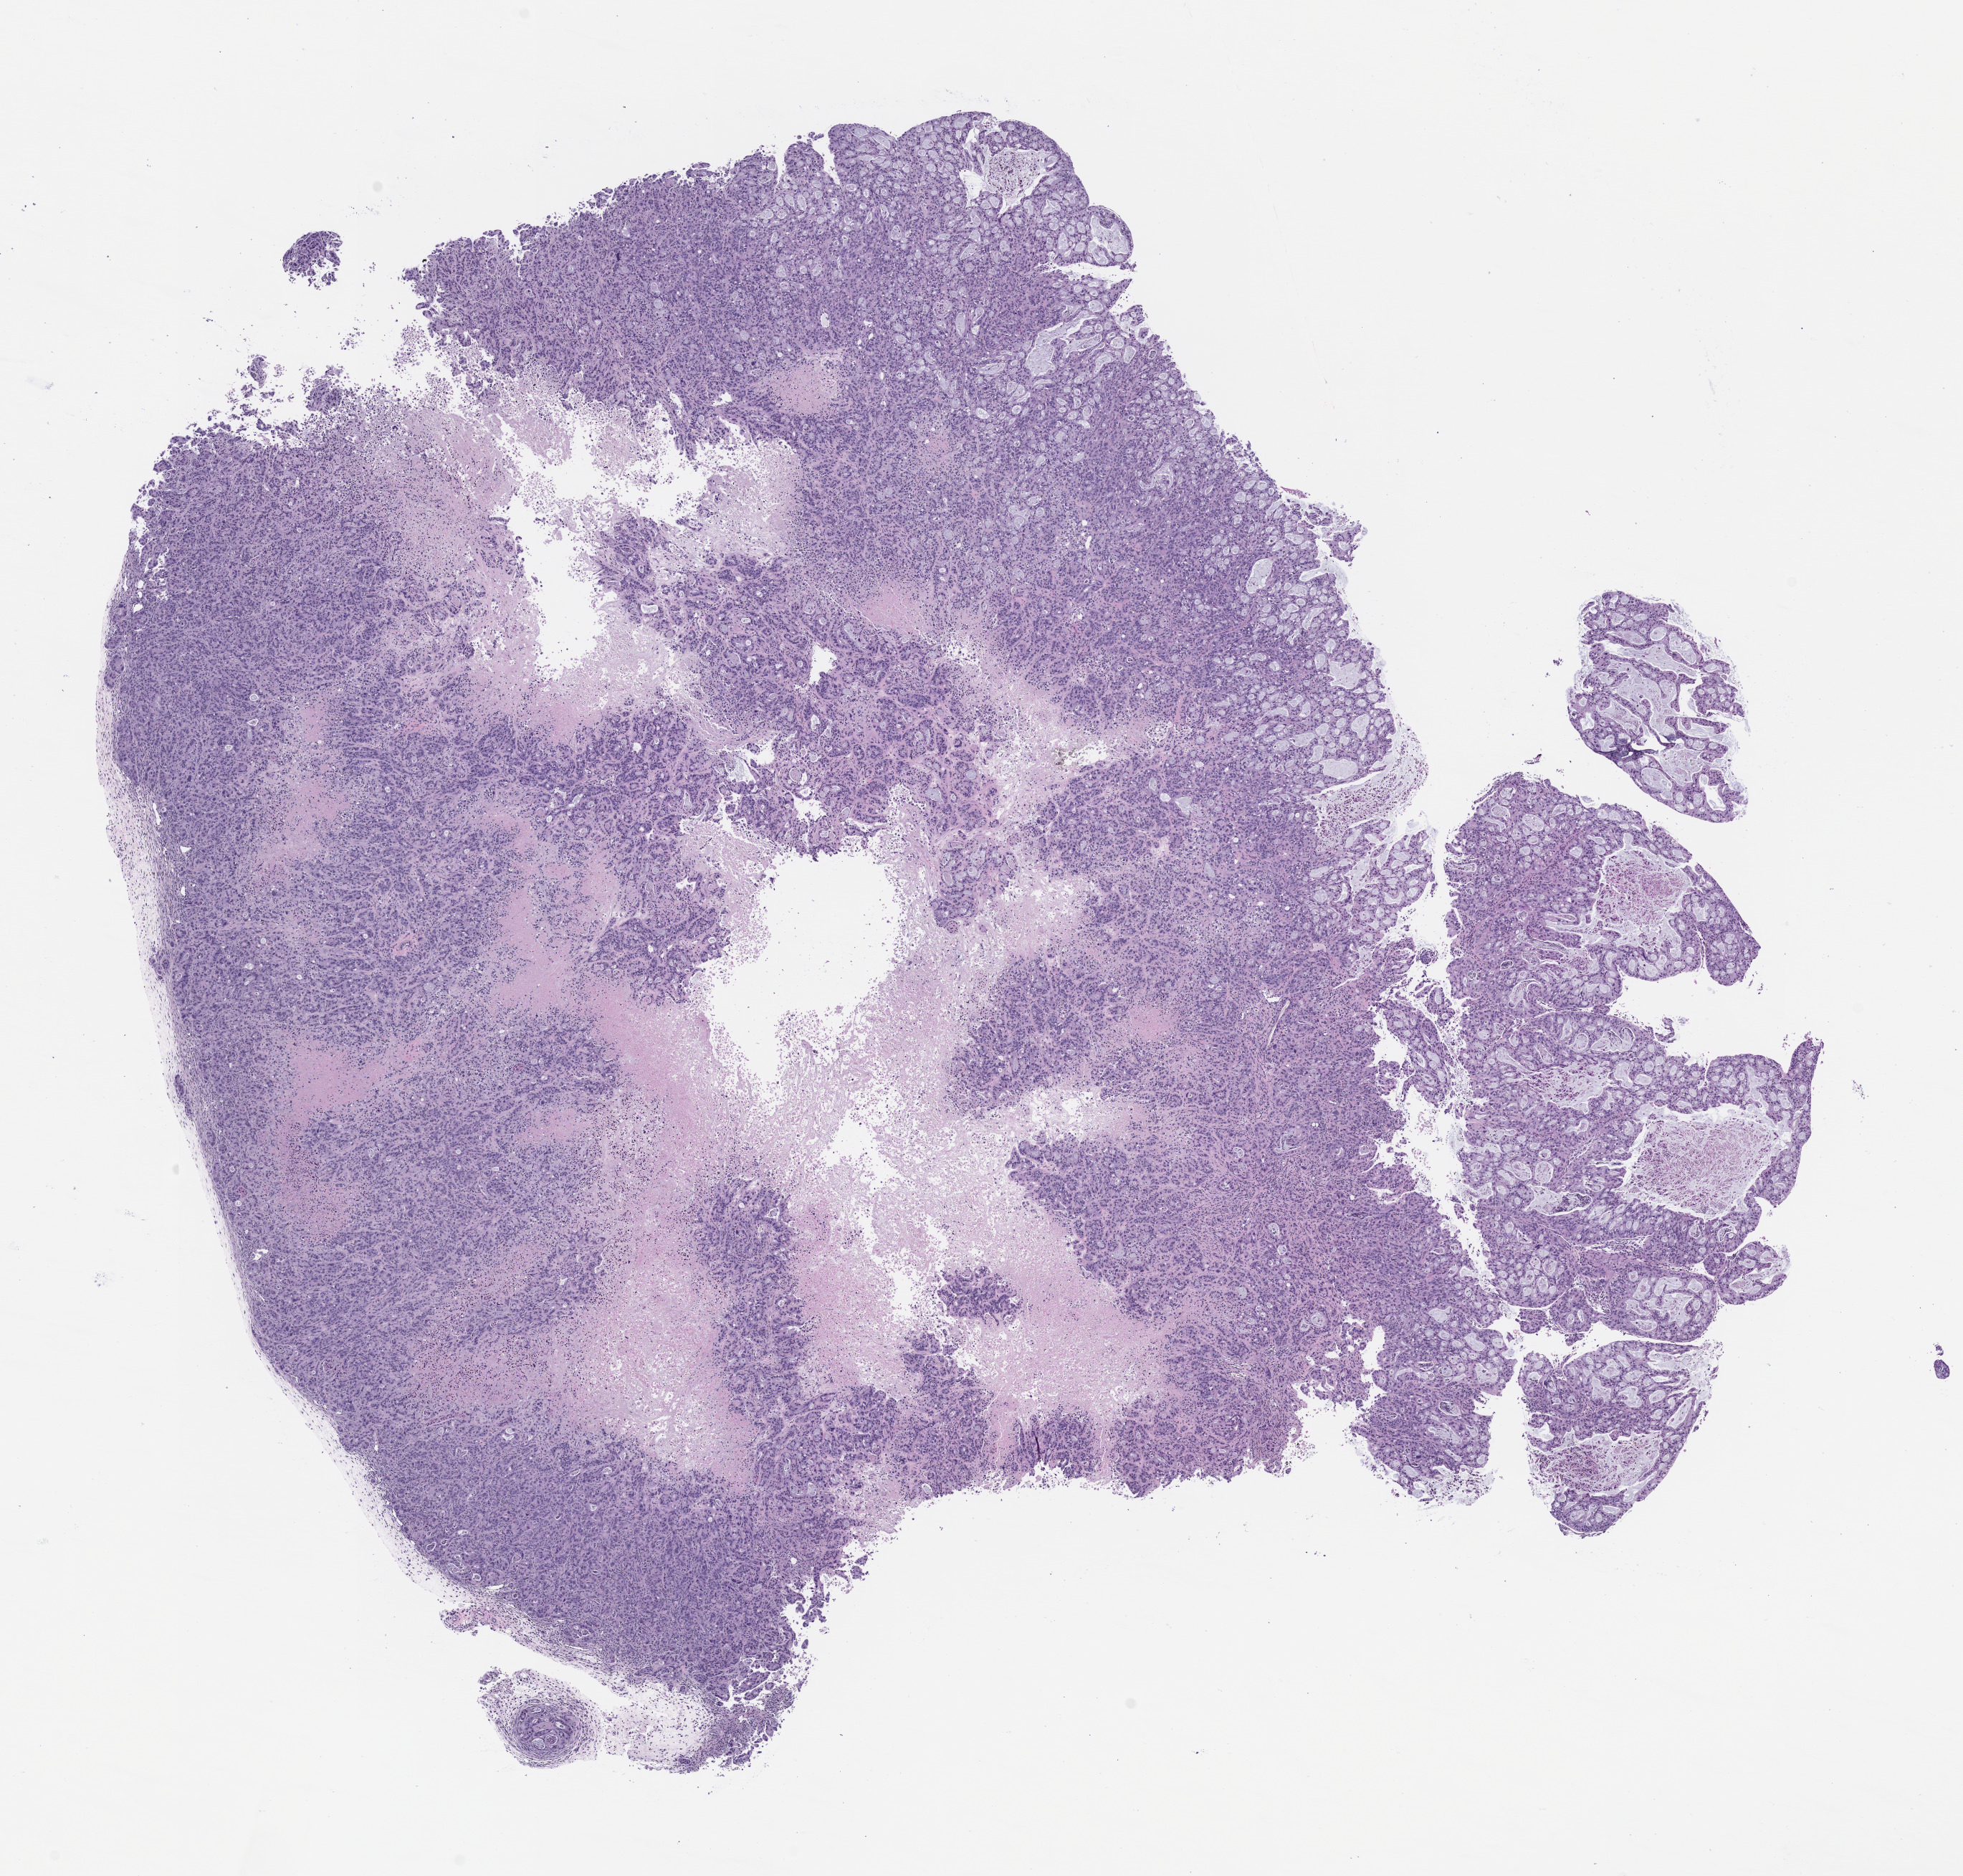
Hematoxylin and eosin (H&E) whole-slide image of a patient-derived xenograft (PDX) tumor grown in a mouse, passage 2 — a low-resolution overview of the entire scanned area, about 11.0 x 10.5 mm. FFPE section. Tumor site category: pancreas.
Originating patient diagnosis: Pancreatic Adenocarcinoma.